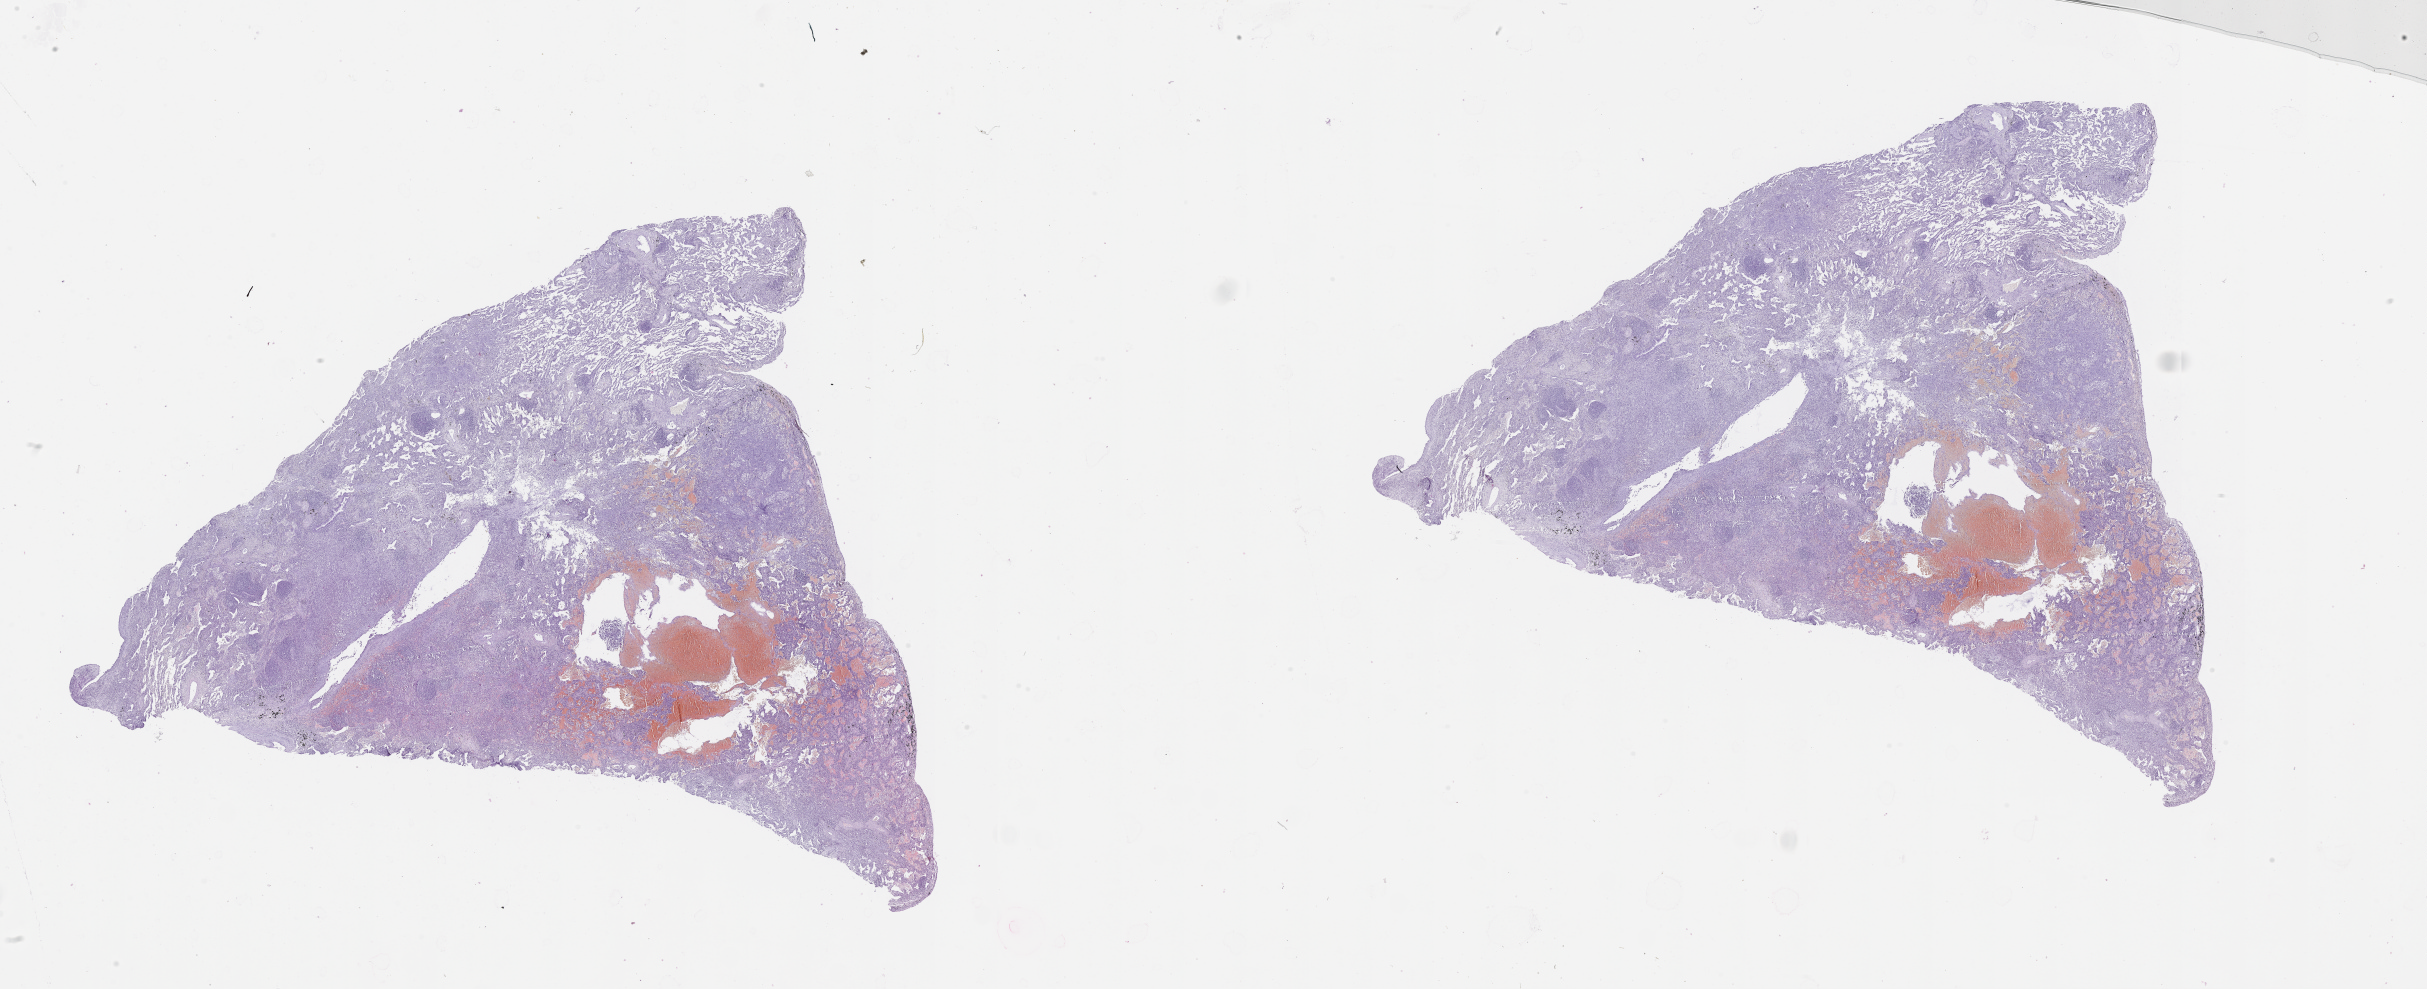
Digitized Hematoxylin and eosin (H&E) stained tissue section (whole slide), low-resolution overview of the scanned area, about 39.1 x 15.9 mm, tumour tissue sample, lung. Male, 70 y/o.
Patient diagnosis (cohort enrolment): squamous cell carcinoma (lung).